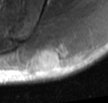
MRI of an extremity soft-tissue mass, one axial slice; slice 13 of 42 in the series (ordered by position); T2-weighted fat-saturated; MR volume resampled by the dataset authors to the PET/CT grid (not the native acquisition matrix); 3.27 mm slice thickness; 108 × 103 image matrix, field of view 105 × 101 mm. Male patient. Case-level facts recorded for this patient, not image findings: histological type: leiomyosarcoma; grade: intermediate; site of the primary tumour: left pelvis.
Structures marked on this image (expert contour drawn on MRI and transferred to this co-registered scan by the dataset authors):
- gross tumour volume (mass): bounding box <34,44,68,72> (left, top, right, bottom; pixels)